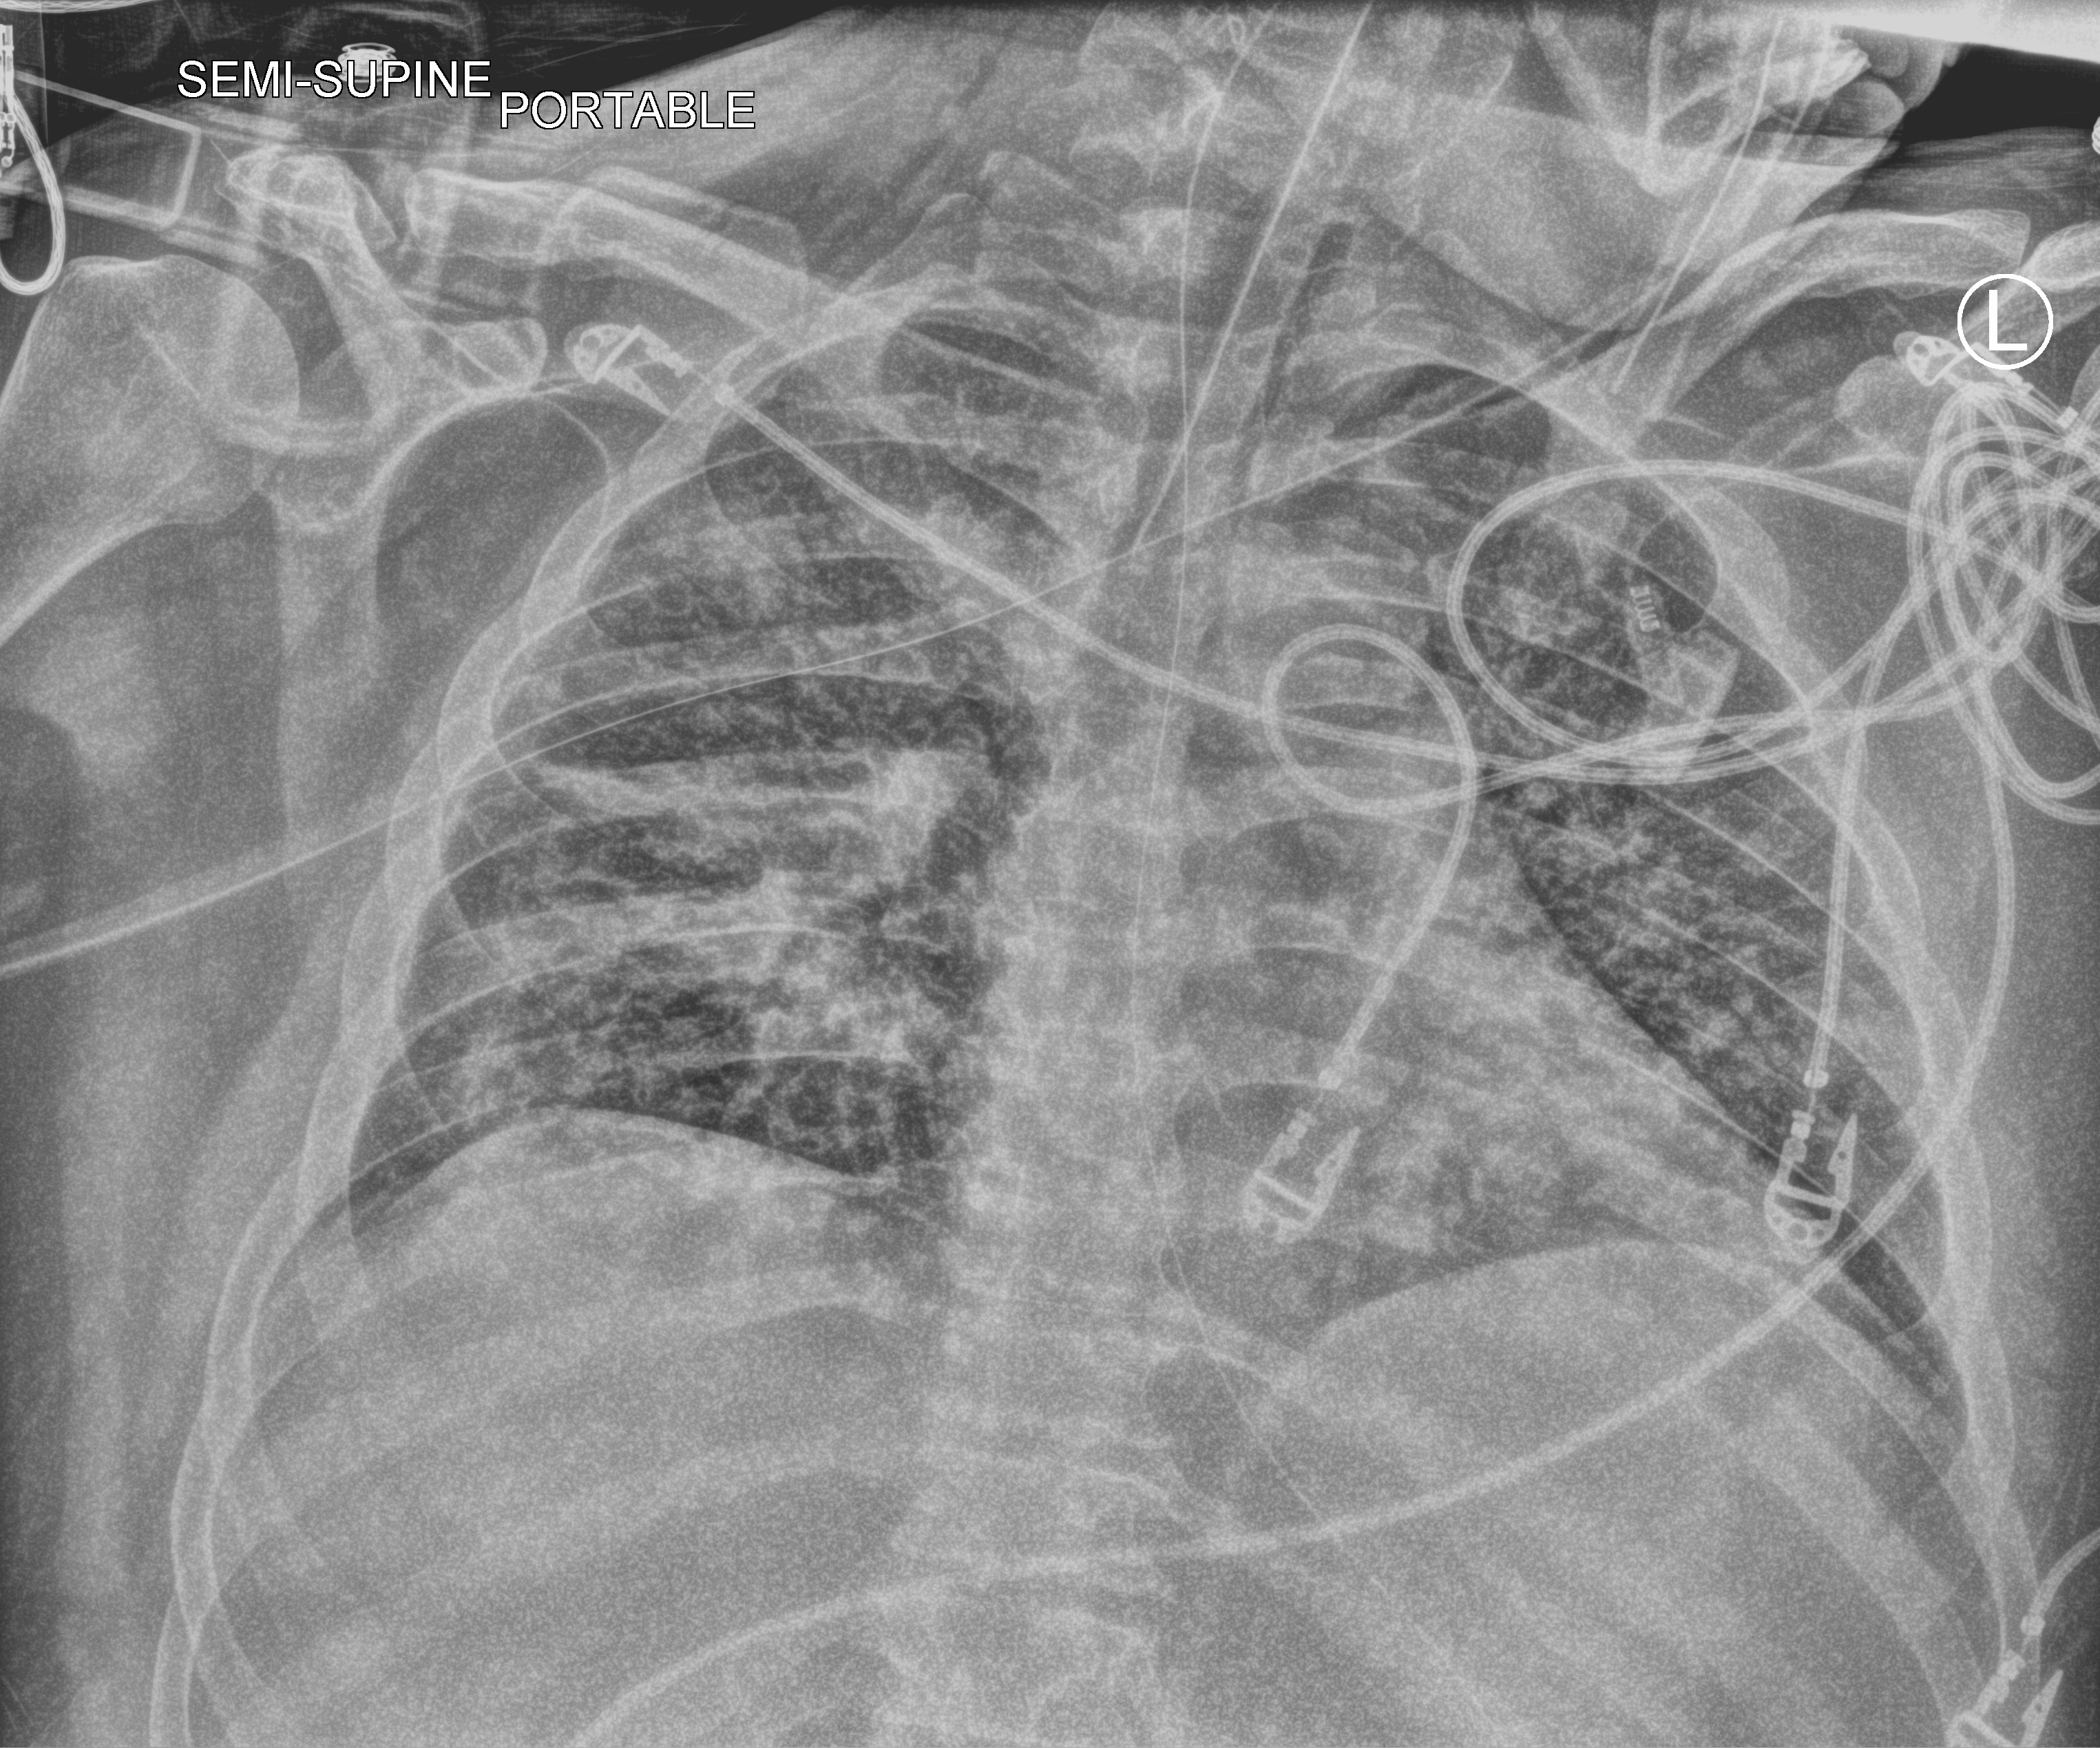
Bedside chest radiograph (computed radiography); anteroposterior (AP) projection. Adult patient hospitalised with COVID-19, age 18–59 years.
Admission-level facts for this patient (not findings on this image; timing relative to this image not recorded):
- length of hospital stay: 31 days
- admitted to intensive care during this hospital stay: yes
- mechanically ventilated during this hospital stay: yes